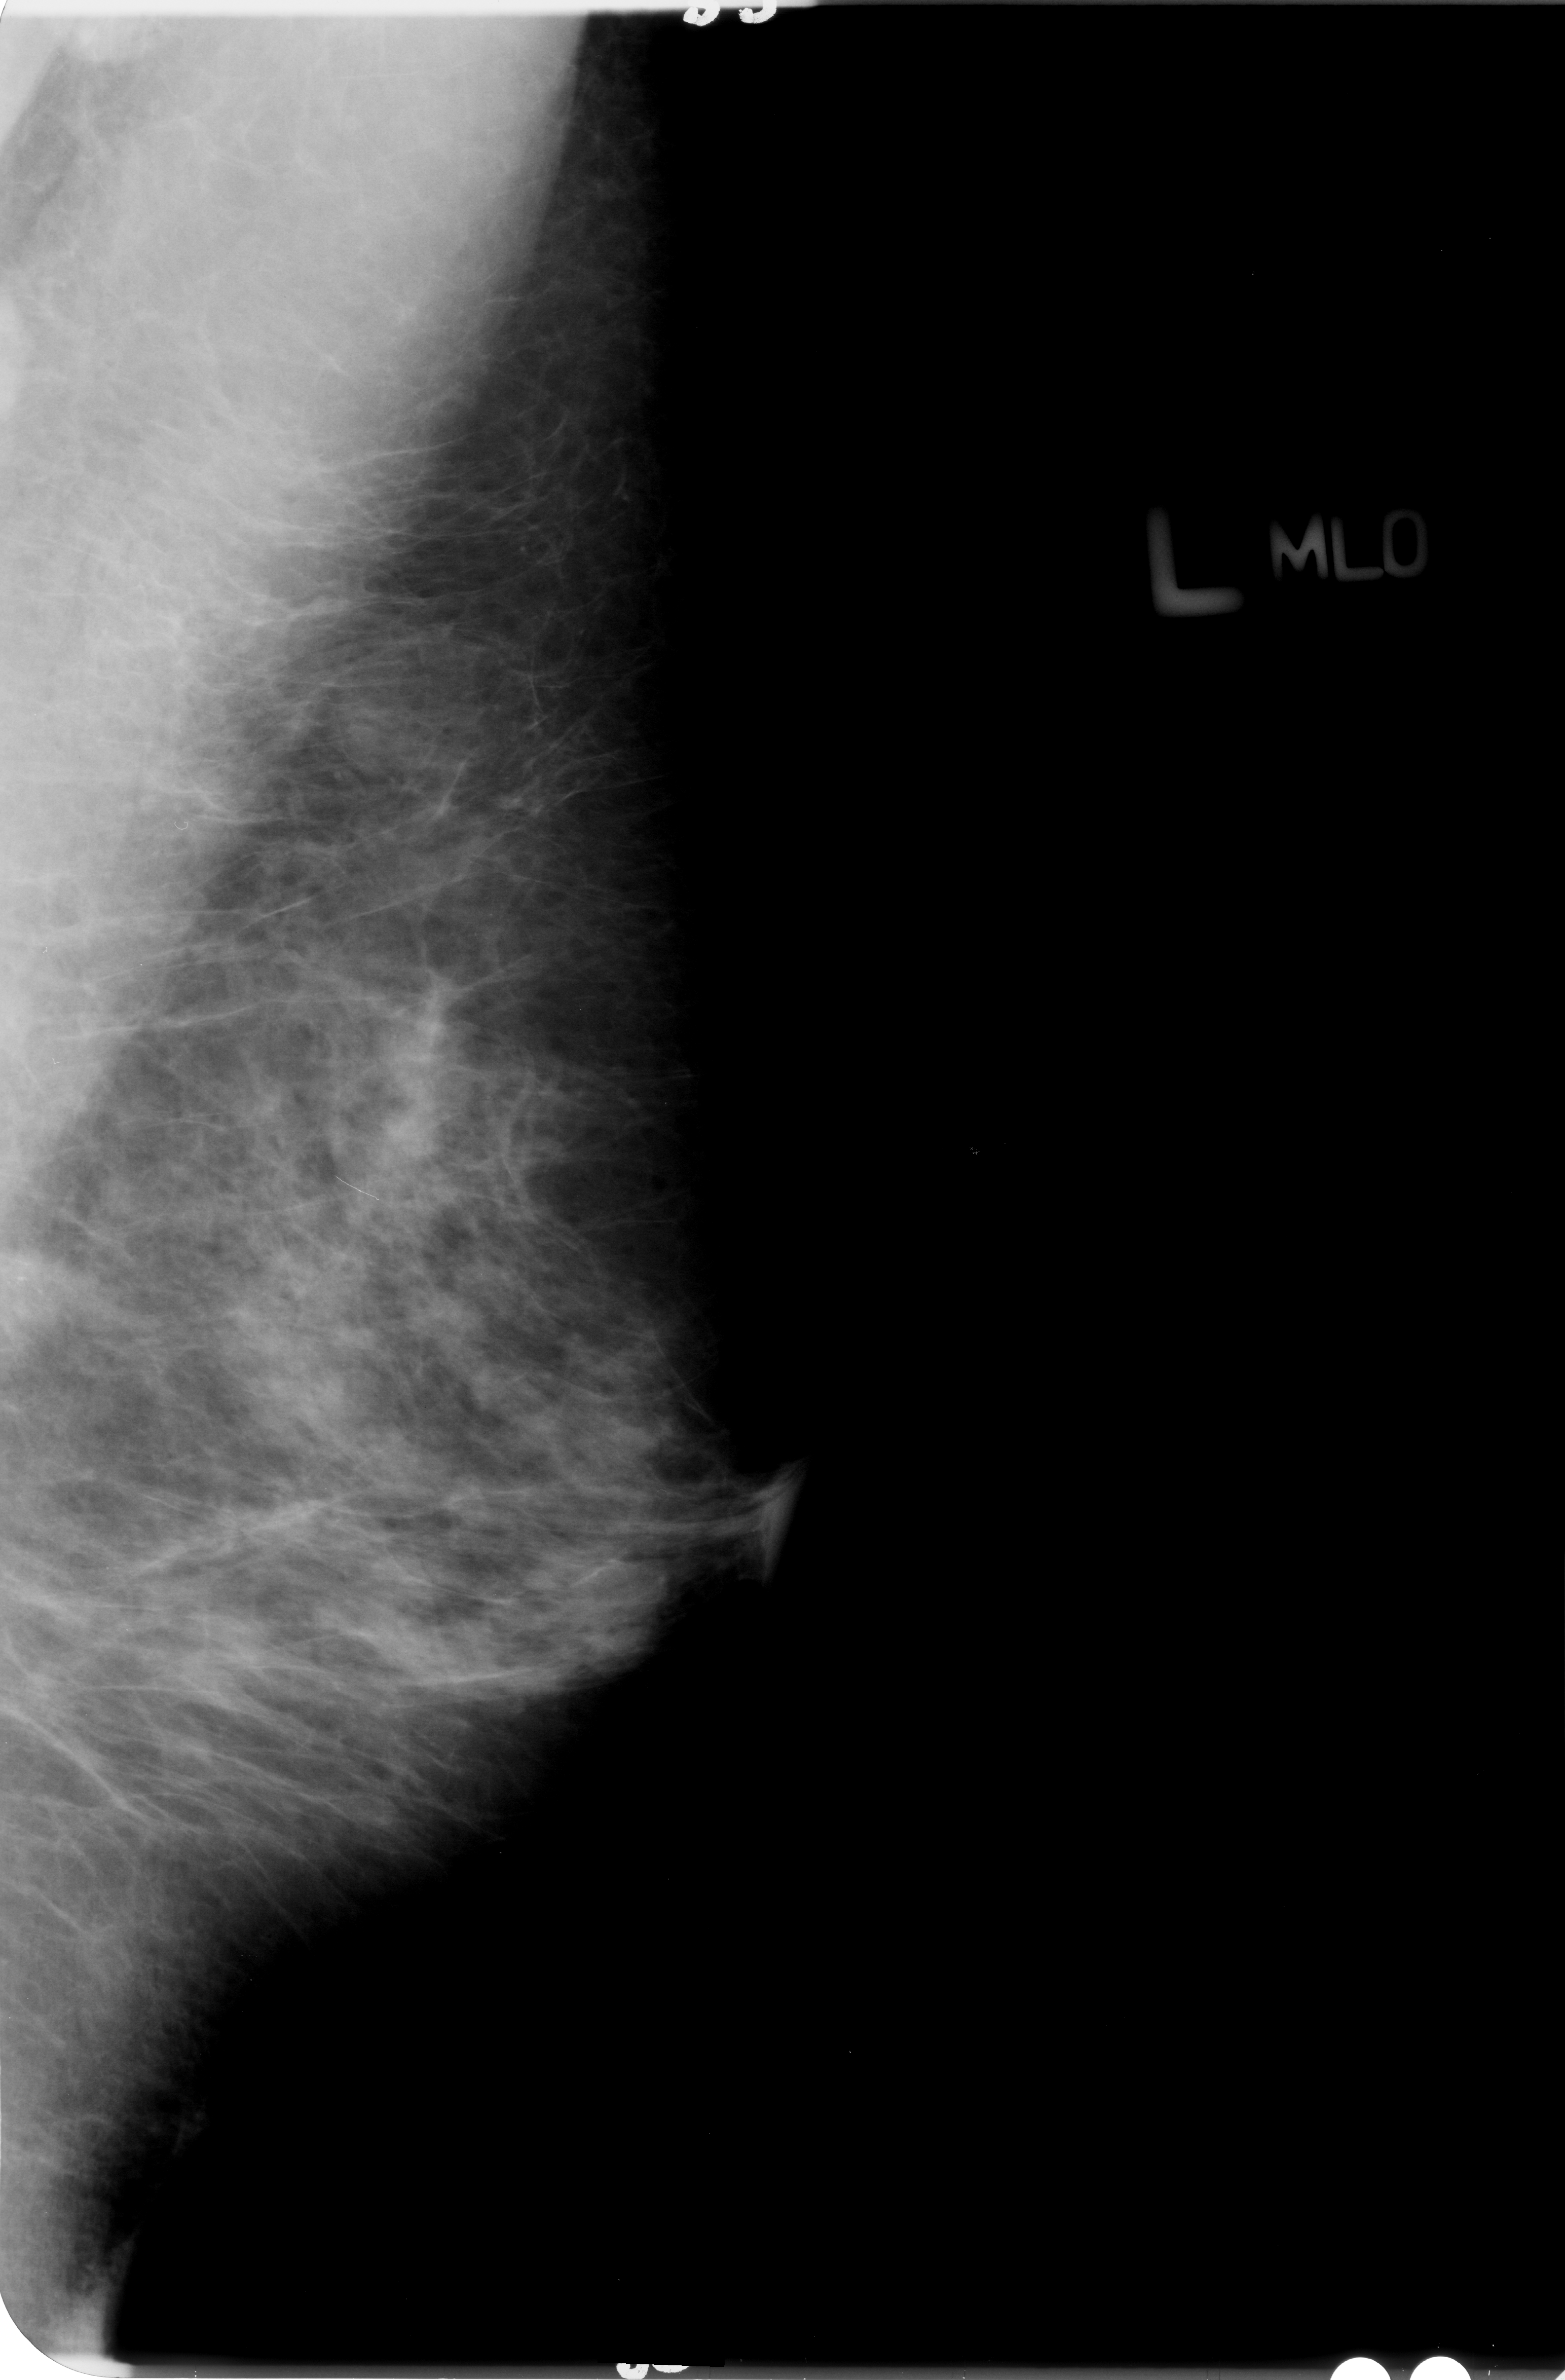
Mammogram (digitized film). Left breast. Mediolateral oblique (MLO) view. BI-RADS breast density category 3 (scale 1–4). 1565 × 2380 image matrix.
Marked abnormalities (boxes around the expert regions of interest):
- calcifications, morphology amorphous / pleomorphic, distribution clustered; BI-RADS assessment category 4; pathology (as recorded): malignant: bounding box (x1, y1, x2, y2) in pixels: (0, 1240, 98, 1339)